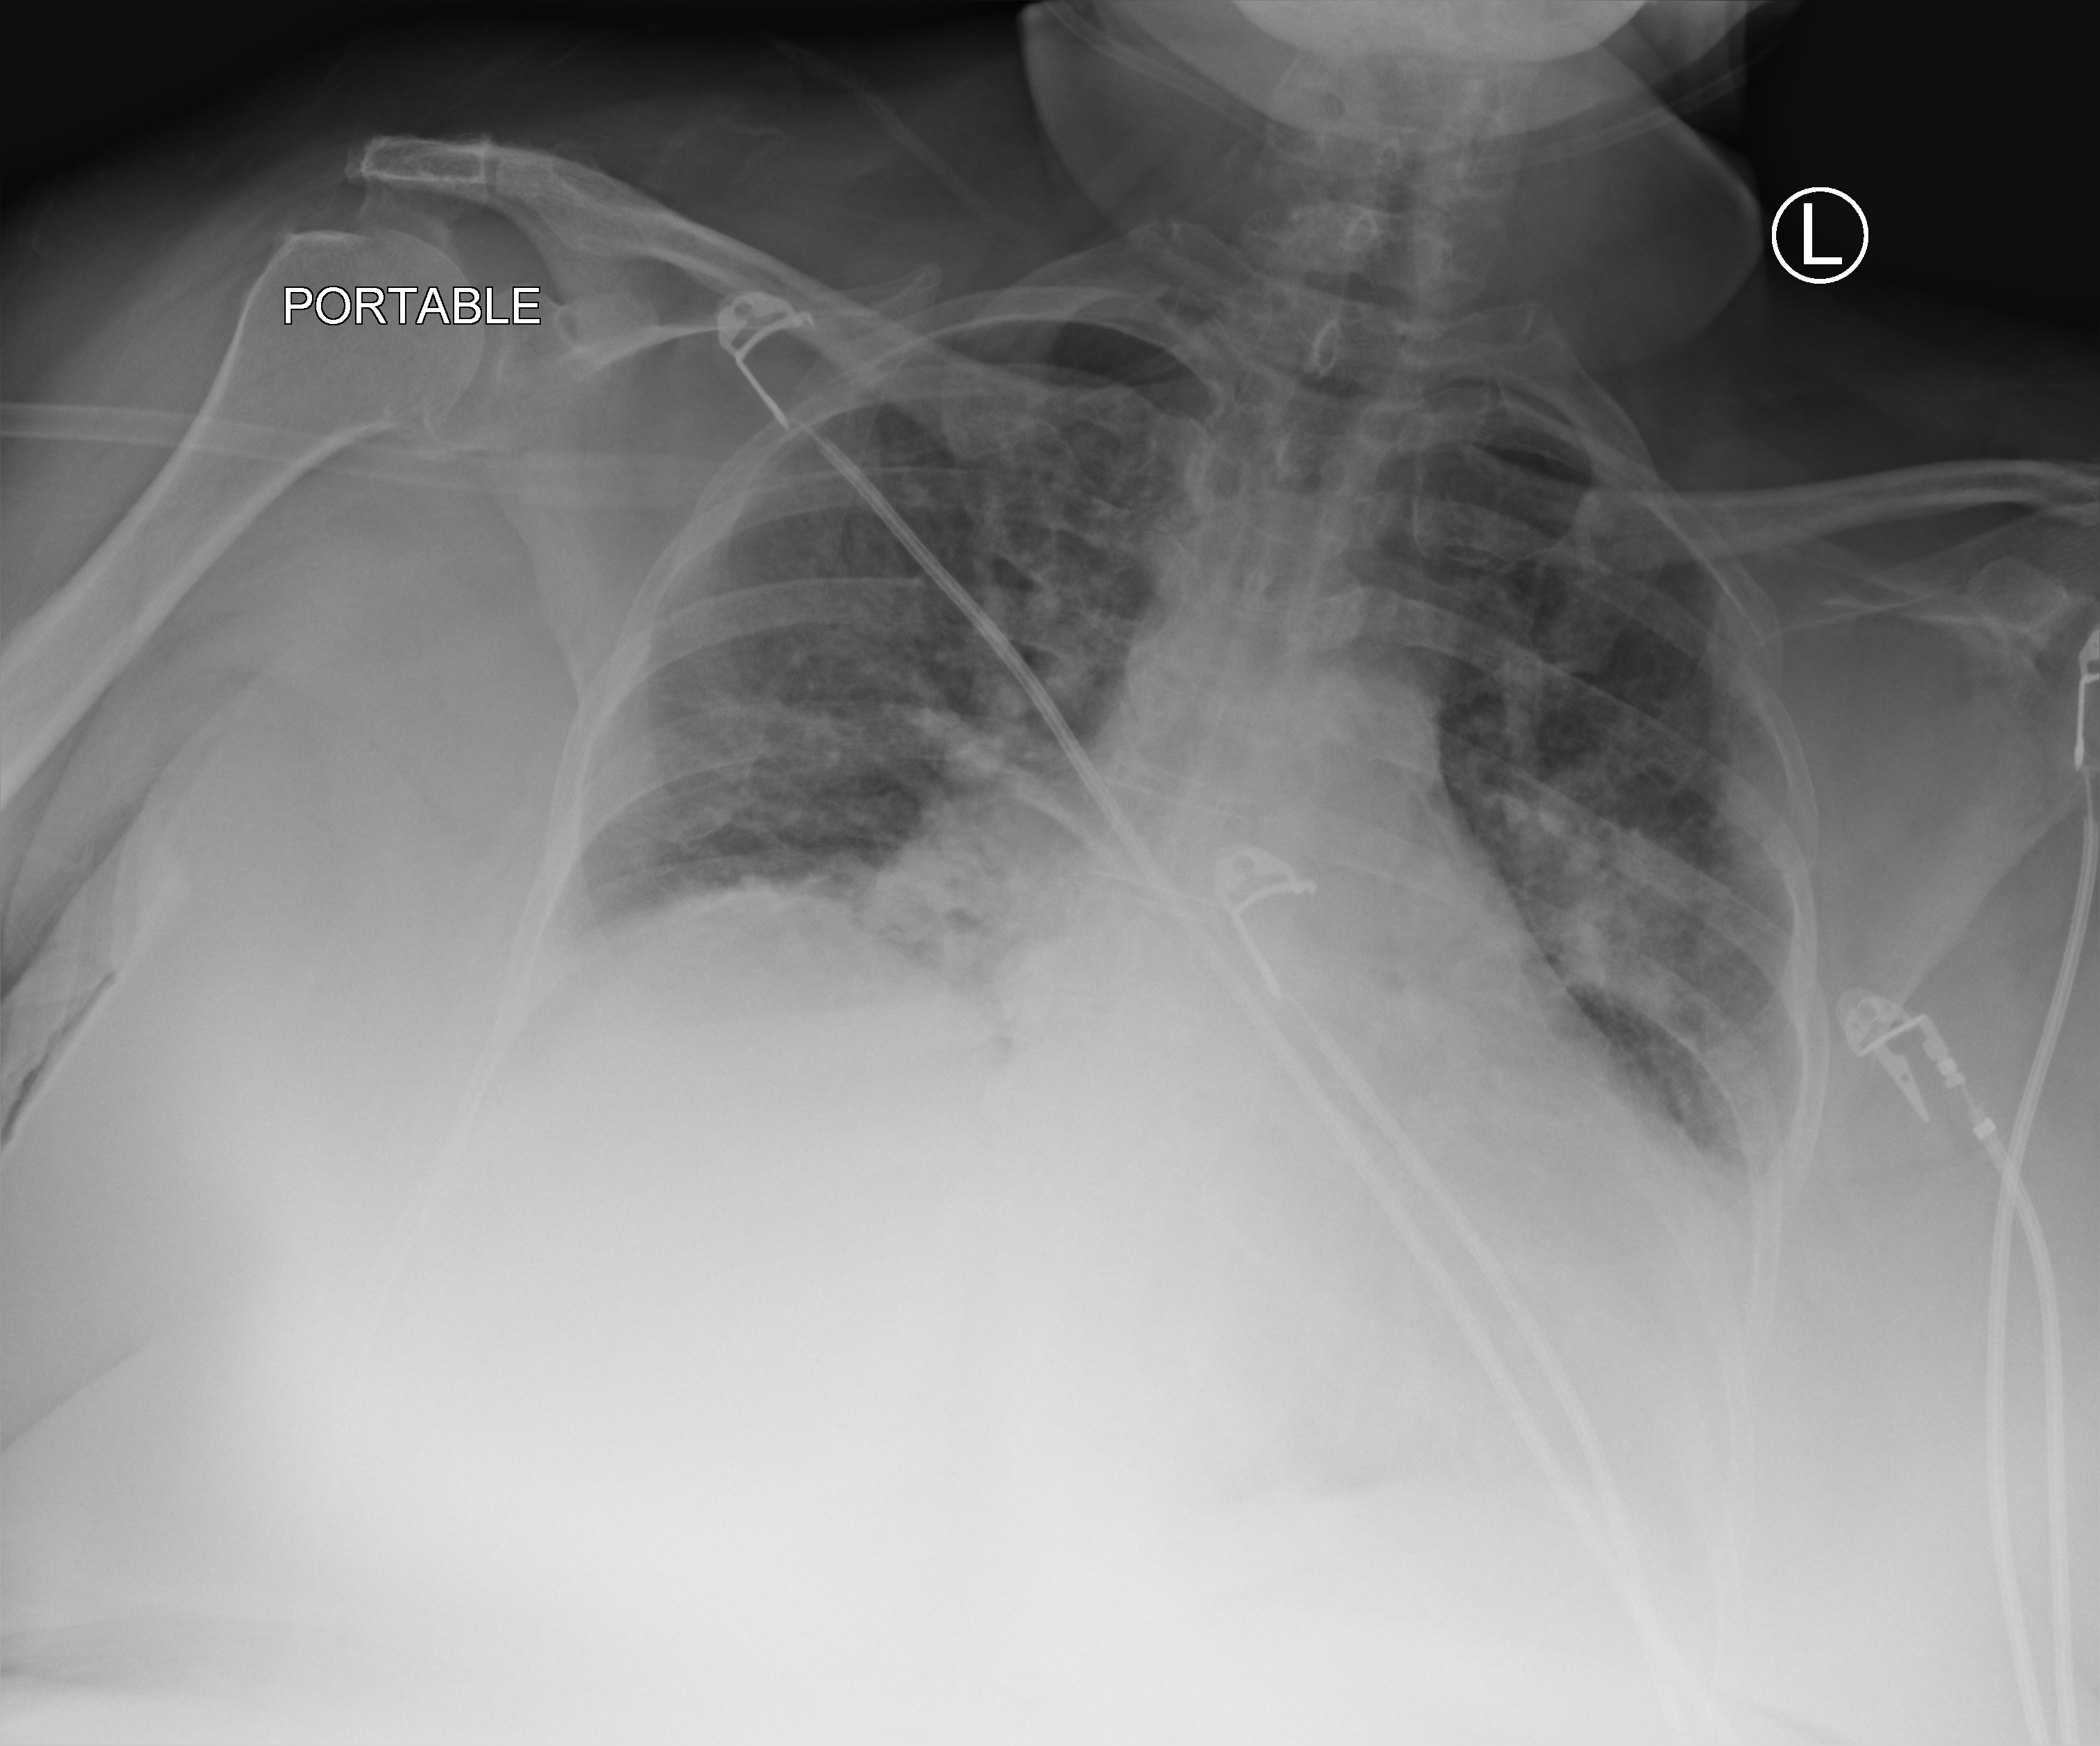
Chest X-ray (portable); anteroposterior (AP) projection. Patient hospitalised with COVID-19; female, aged 60–74 years.
From the hospital-stay record, not from the radiograph (when in the stay this image was taken is not recorded): hypertension (admission record): yes.